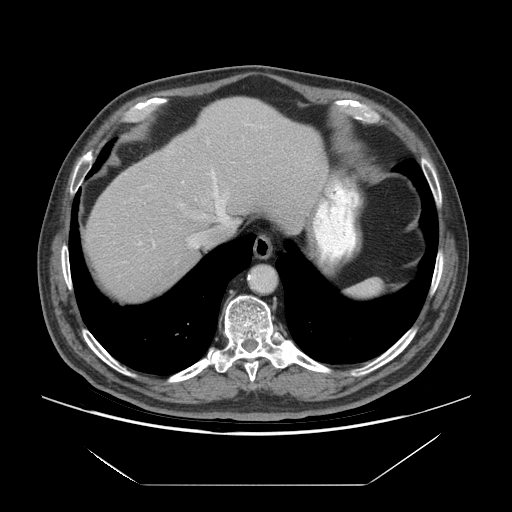
Contrast-enhanced abdominal CT (liver protocol), one axial slice. Slice 59 of 75 in the series (ordered by position). Reconstruction kernel STANDARD. 140 kVp. Soft-tissue window (W 400 / L 40 HU). 2.5 mm slice thickness. 512 × 512 image matrix, field of view 420 × 420 mm. Case-level facts recorded for this patient, not image findings: diagnosis: hepatocellular carcinoma (patient treated with transarterial chemoembolisation; whether this scan precedes or follows treatment is not stated here); TNM stage (as recorded): Stage-I; Child-Pugh class: A; tumour differentiation: well differentiated; tumour nodularity: uninodular.
Annotated regions visible in this slice (semi-automatically segmented with operator editing):
- abdominal aorta: bounding box <250,267,275,291> (left, top, right, bottom; pixels)
- liver parenchyma outside the tumour (the mass and vessels are separate outlines, so this box may not span the whole liver): <84,98,328,298>
- liver vessels: <138,124,261,247>